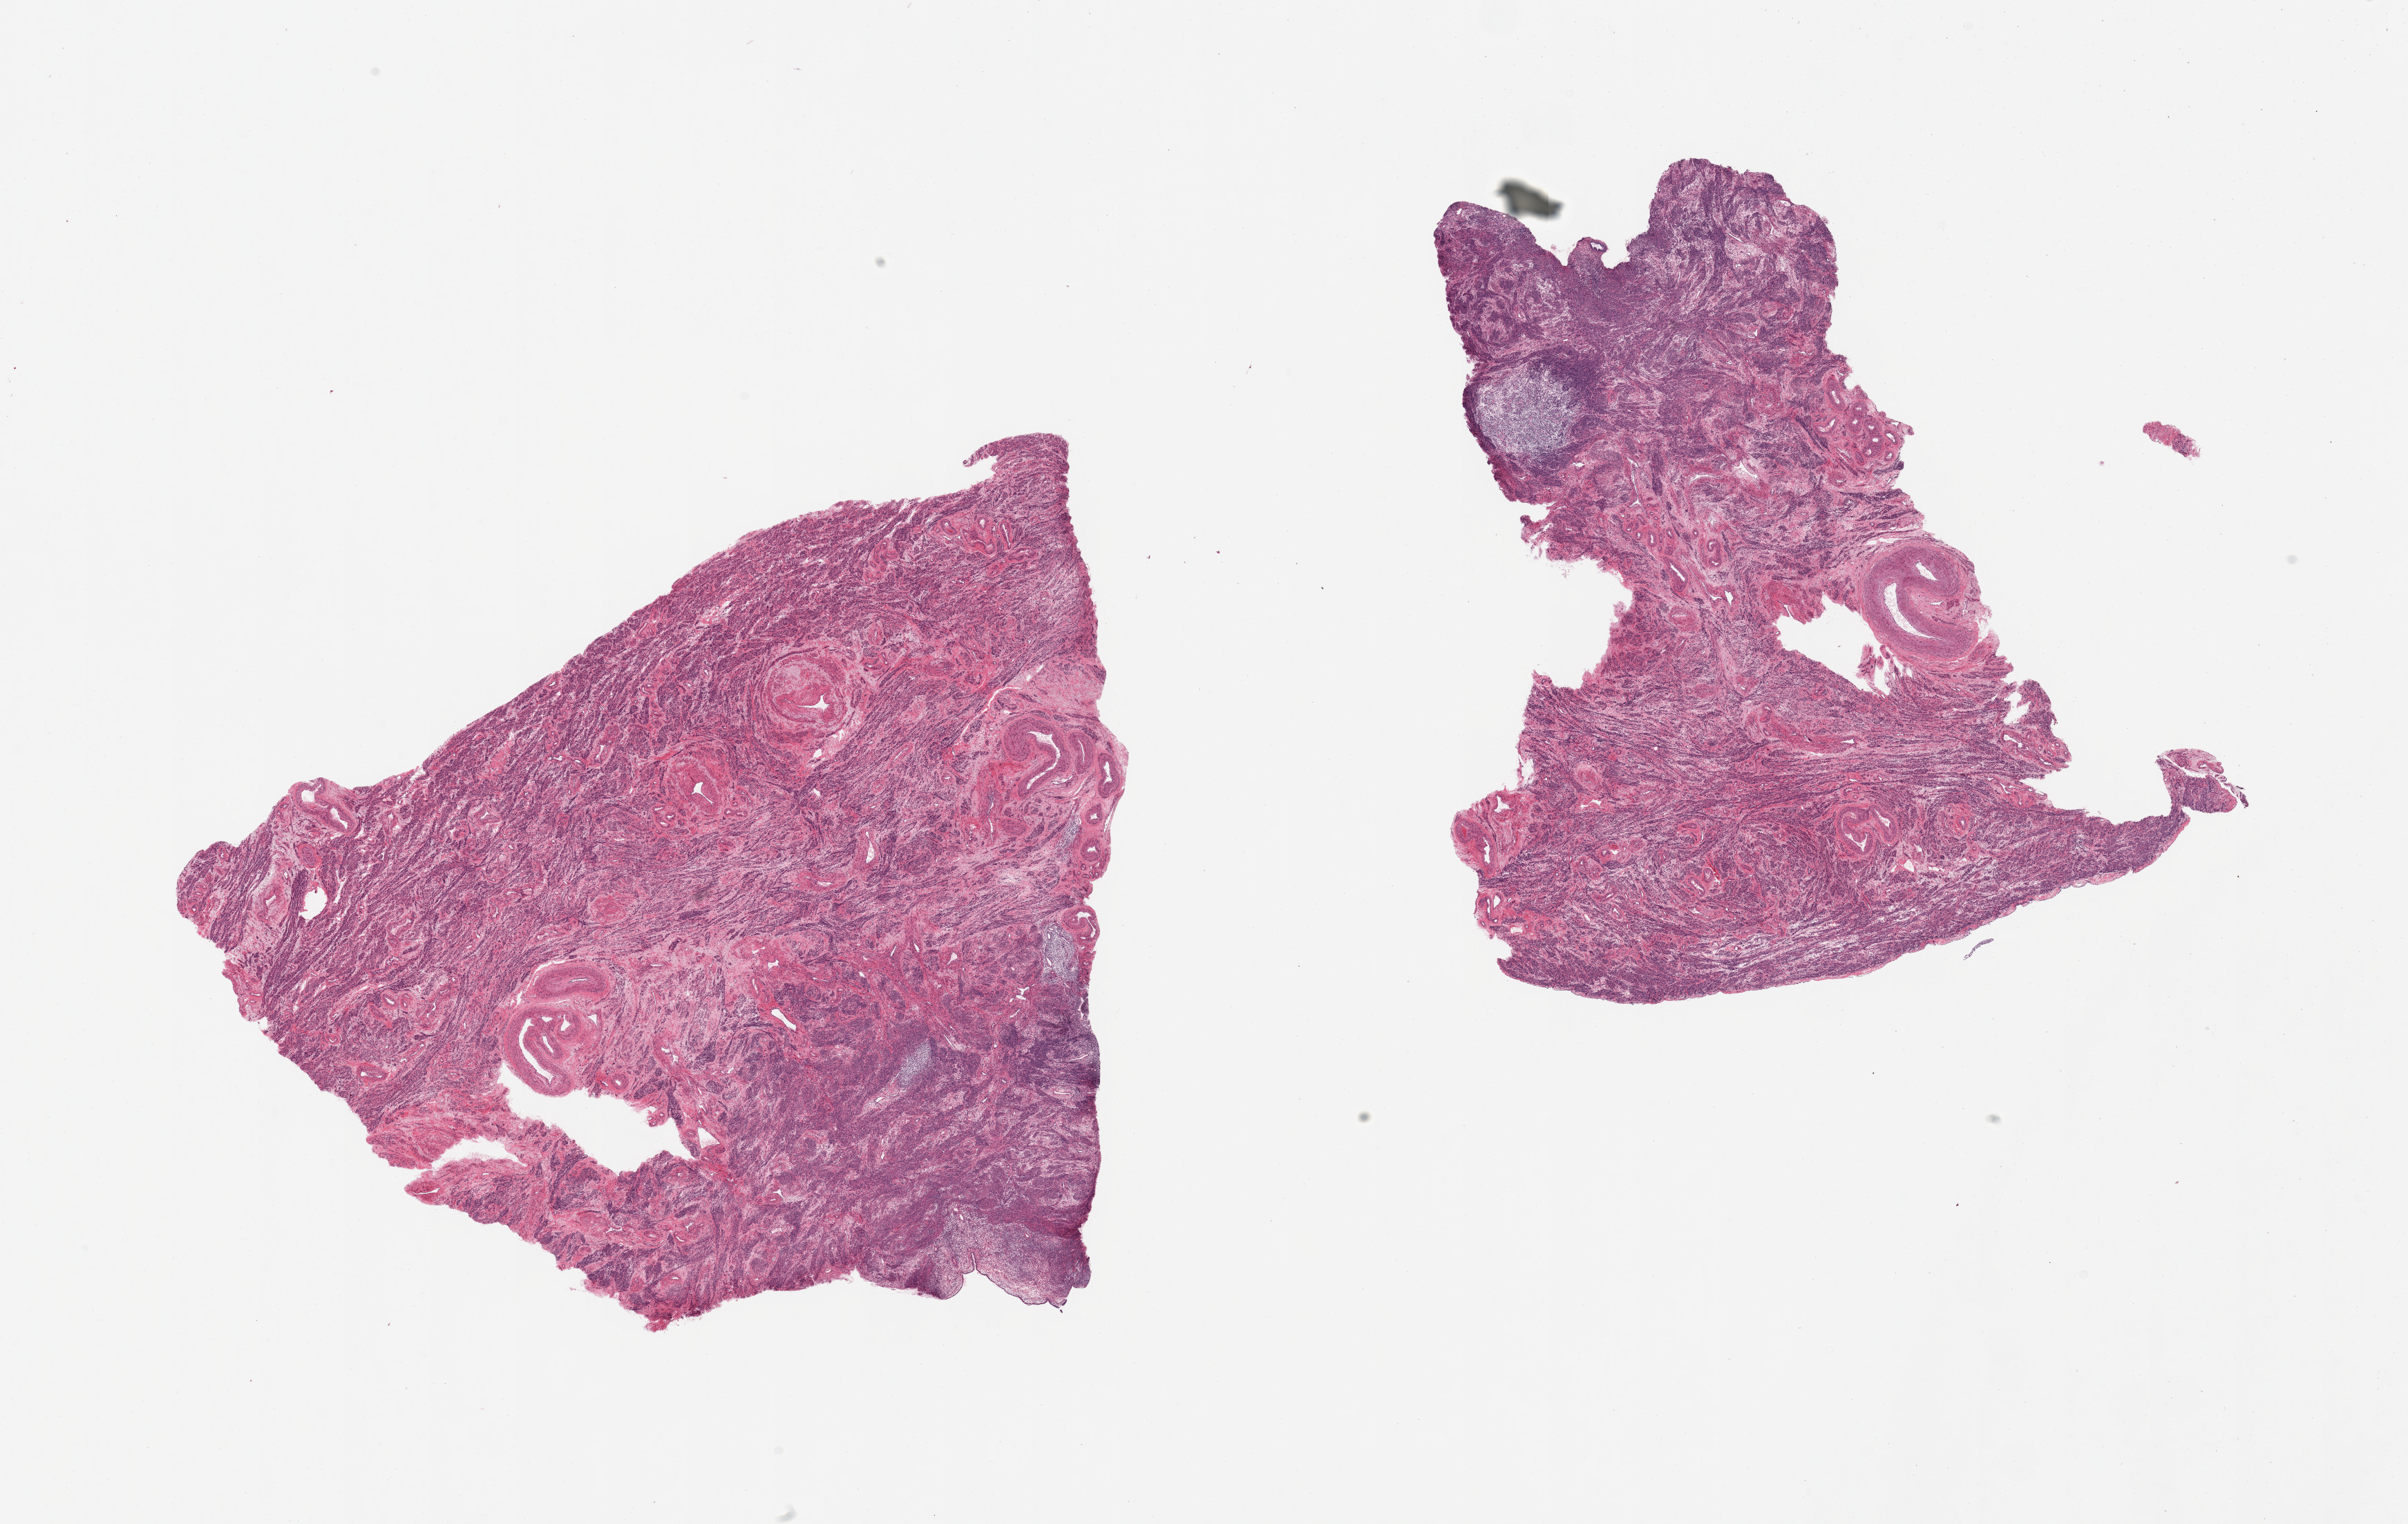
Digitized hematoxylin and eosin (H&E)-stained section, brightfield — shown as a low-resolution overview of the whole scanned area (about 27.6 x 17.4 mm), PAXgene-fixed paraffin-embedded (PFPE) section, sampled site (target tissue): uterus, donor tissue sample. Donor sex: female.
Review note (as recorded): 2 pieces, microscopic endometrial stromal nodule.